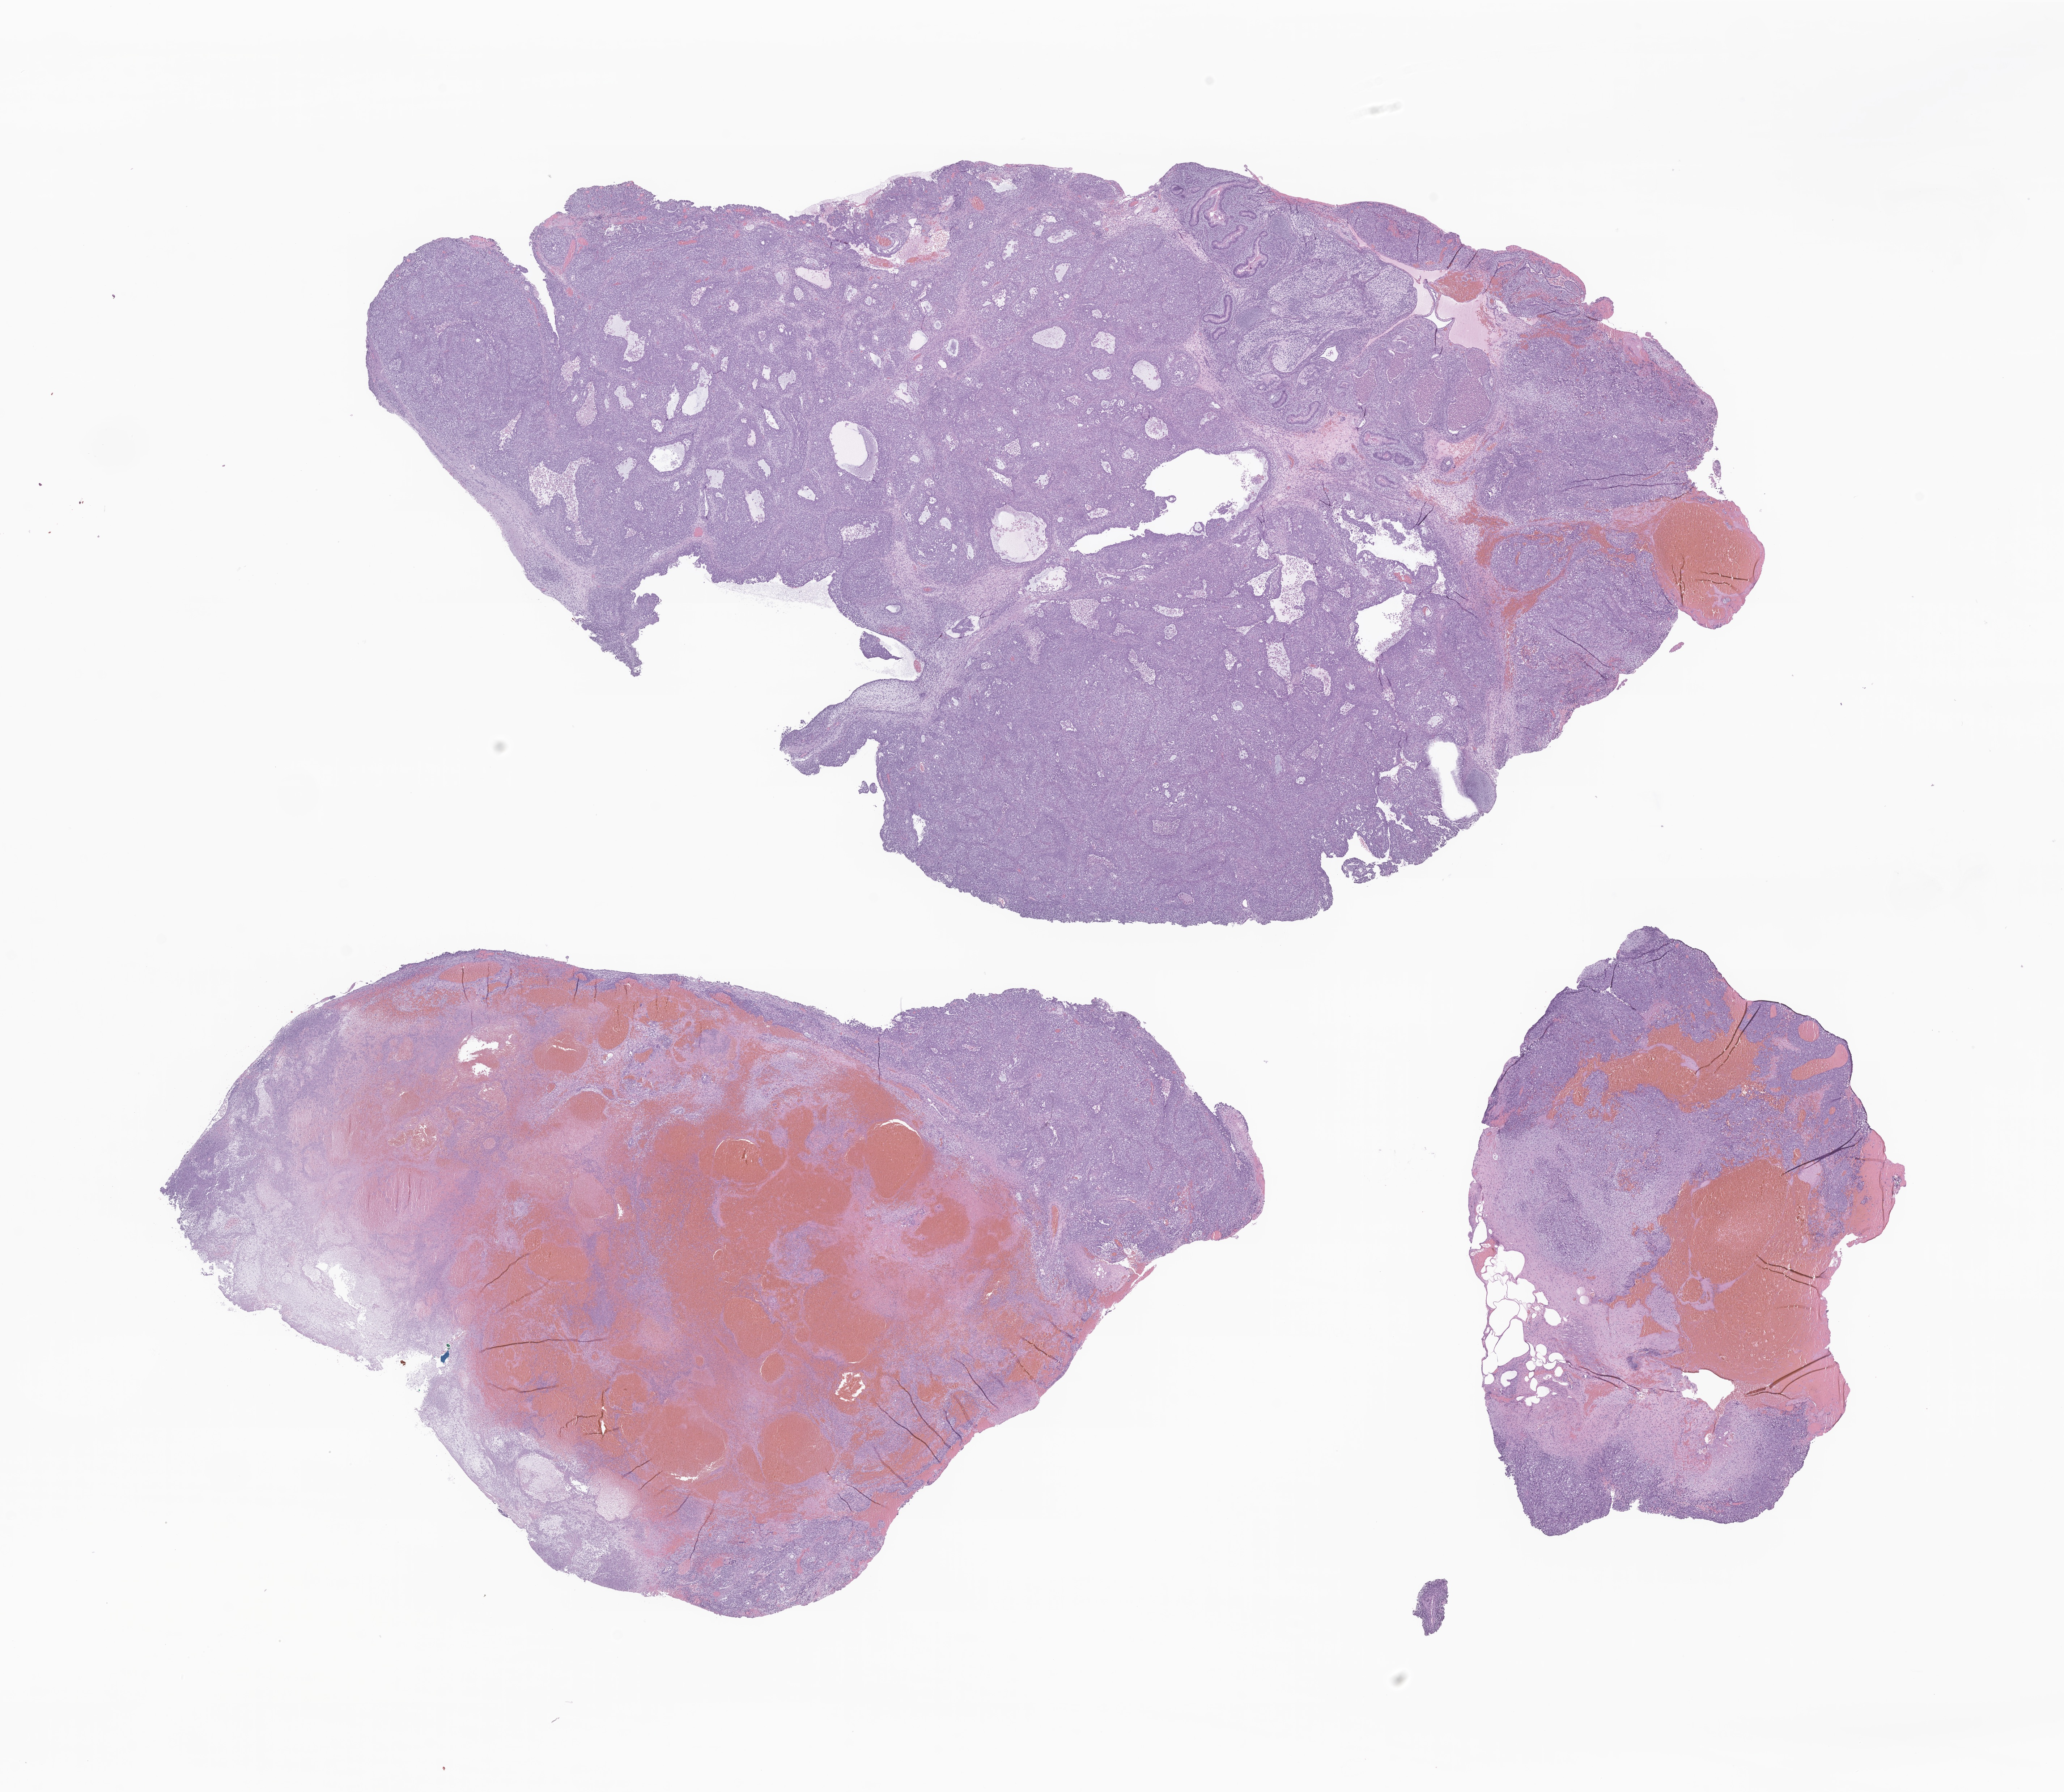
Digitized H&E-stained section of tumor tissue from the brain, whole scanned area (about 24.1 x 20.9 mm) shown as a low-resolution overview; FFPE section. Patient male; age 288 months (24 years).
Recorded diagnosis: Mixed germ cell tumor.